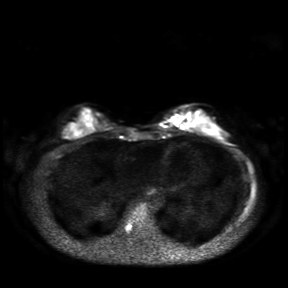
Breast MRI, one axial slice. Position 9 of 30 along the scan axis. Diffusion-weighted series; image 2 of 4 stored at this slice position (different b-values; order by instance number). 3 T. 4 mm slice thickness. 288 × 288 image matrix, field of view 360 × 360 mm. Female patient.
Outlined on this slice (expert manual segmentation):
- tumour on diffusion-weighted imaging: bounding box <171,115,180,121> (left, top, right, bottom; pixels)